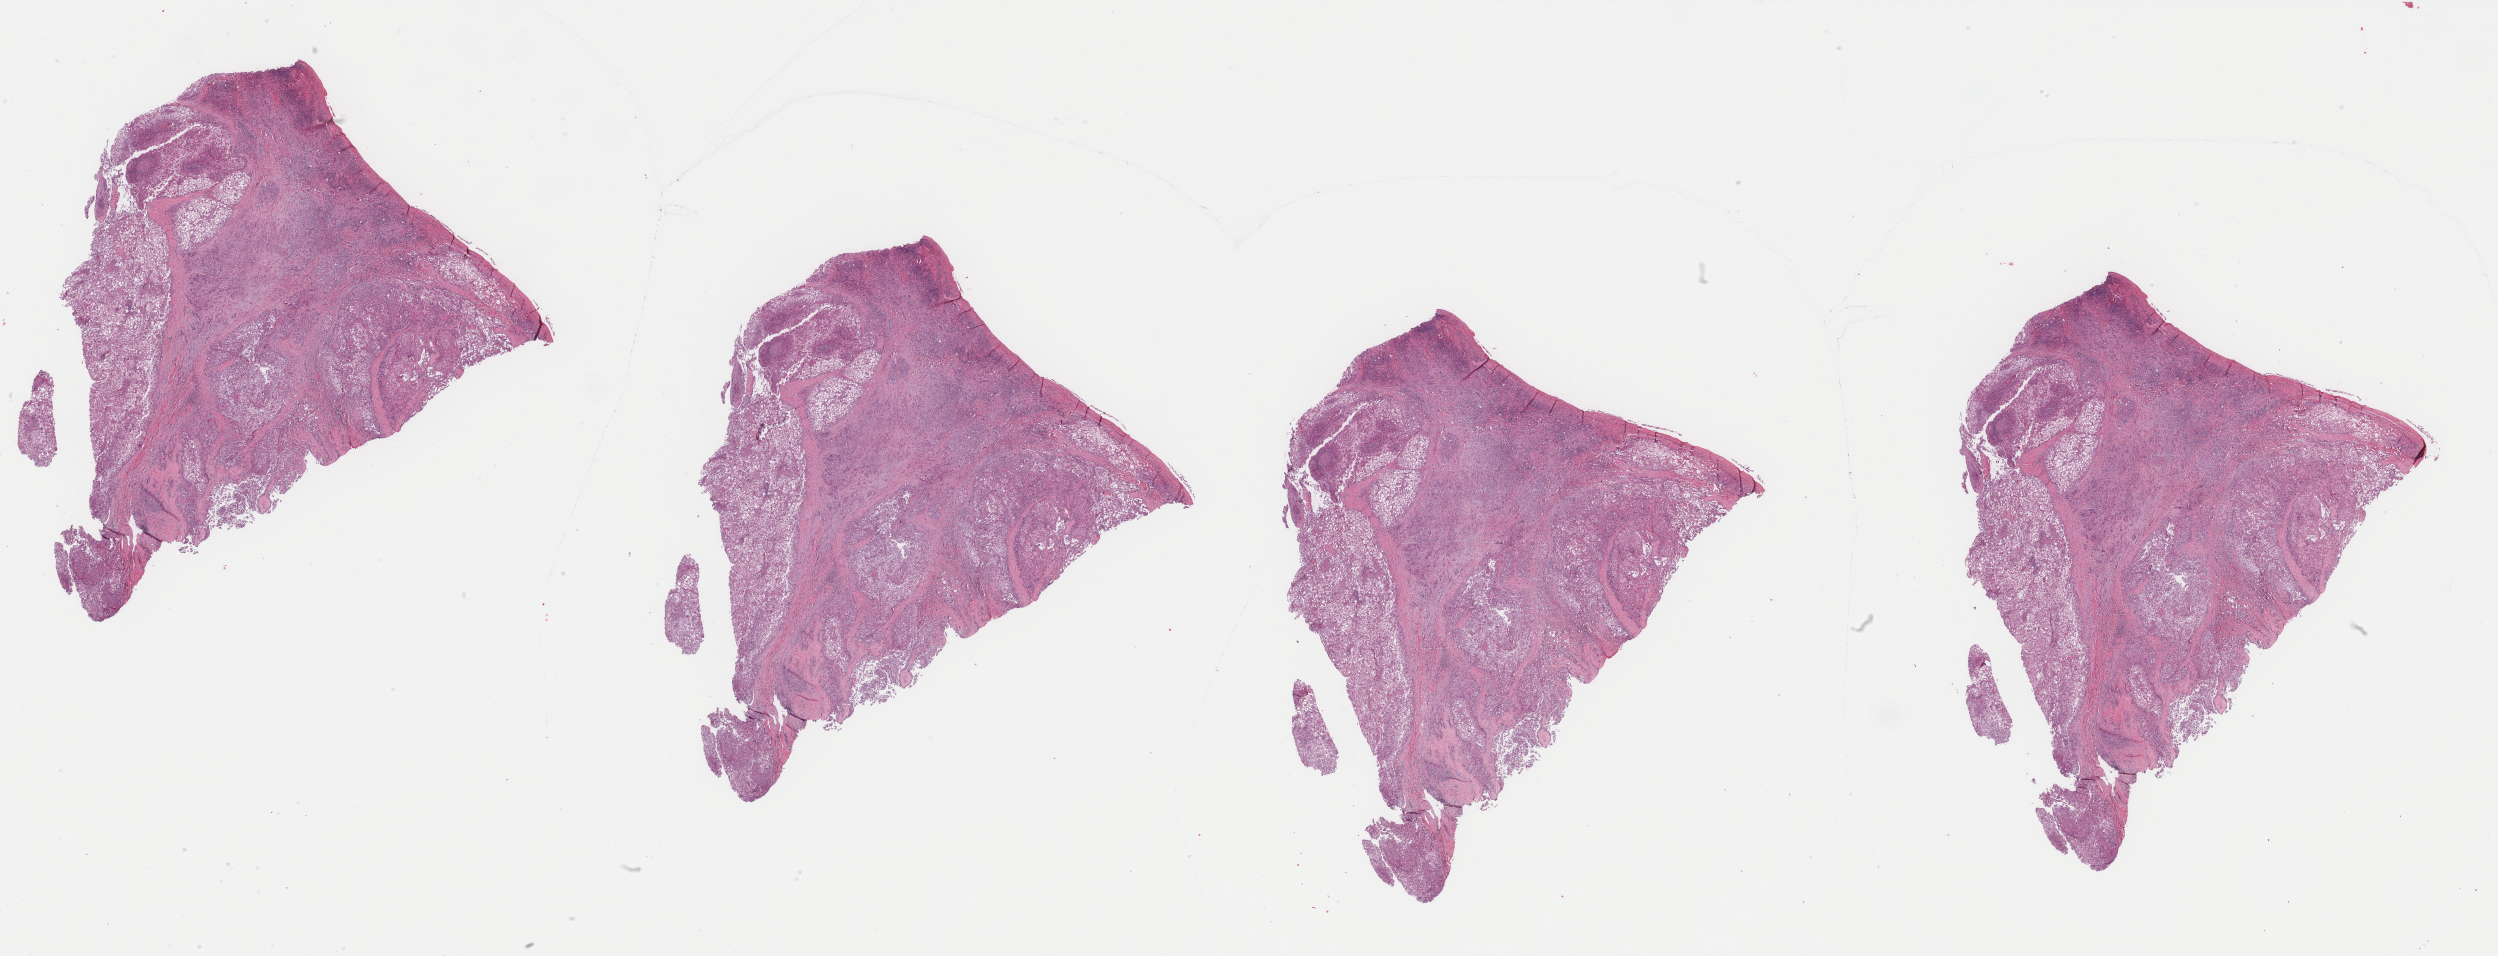
Digitized H&E-stained tissue section (whole slide) — shown as a low-resolution overview of the whole scanned area (about 39.7 x 15.2 mm); formalin-fixed paraffin-embedded (FFPE) diagnostic section; liver, primary tumour sample. Male patient; age at initial diagnosis 59 years. Histologic grade: G2 (moderately differentiated).
Histologic diagnosis: Hepatocellular carcinoma, clear cell type. AJCC pathologic stage: I (7th edition).